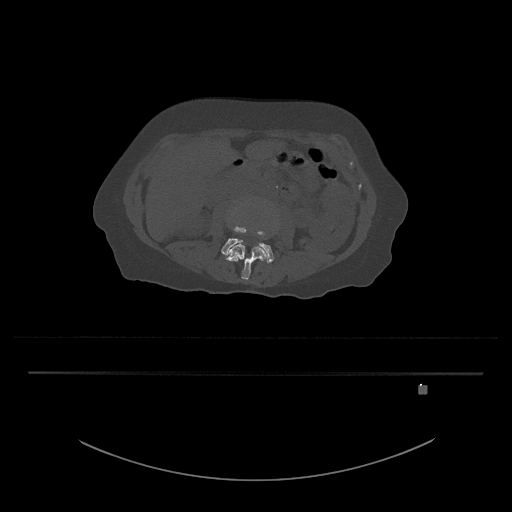
CT including the spine, one axial slice. Position 397 of 797 along the scan axis. Reconstruction kernel Br40s/3. 120 kVp. Bone window (W 1800 / L 400 HU). 0.5 mm slice thickness. 512 × 512 image matrix, field of view 500 × 500 mm. Patient: female, 57 years. From the clinical record (not read from this slice): primary cancer: cervical.
Annotated regions visible in this slice (semi-automatically segmented with operator editing):
- L3 vertebra: box from (x=225, y=229) to (x=267, y=280) px
- L4 vertebra: (x=221, y=213)–(x=274, y=263)